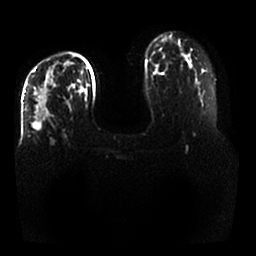
Breast MRI, one axial slice; position 17 of 25 along the scan axis; diffusion-weighted series; image 2 of 4 stored at this slice position (different b-values; order by instance number); 1.5 T; 4 mm slice thickness; 256 × 256 image matrix, field of view 350 × 350 mm. Female patient.
Structures marked on this image (expert manual segmentation):
- tumour on diffusion-weighted imaging: box from (x=32, y=78) to (x=55, y=132) px